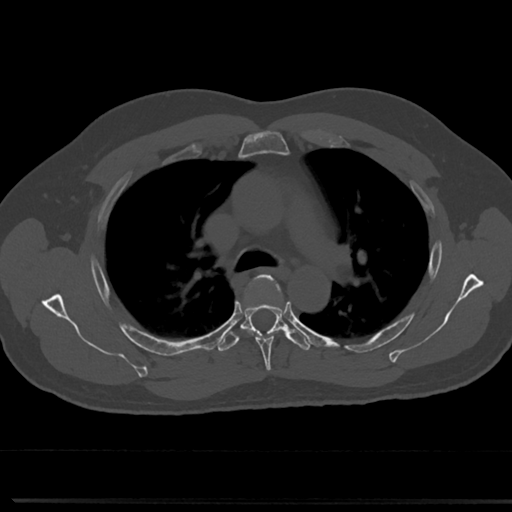
CT including the spine, one axial slice. Position 521 of 817 along the scan axis. Reconstruction kernel Br40s/3. Bone window (W 1800 / L 400 HU). 0.5 mm slice thickness. 512 × 512 image matrix, field of view 355 × 355 mm. Patient: male, 61 years. Case-level facts recorded for this patient, not image findings: primary cancer: prostate.
Structures marked on this image (semi-automatic segmentation, software-assisted and operator-edited):
- T4 vertebra: bounding box [x1, y1, x2, y2] px = [240, 275, 287, 362]
- T5 vertebra: [223, 308, 310, 349]